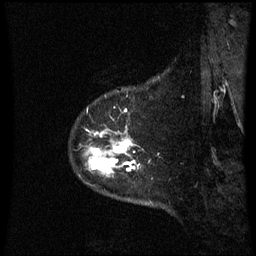
Breast MRI (dynamic contrast-enhanced), one sagittal slice; position 54 of 60 along the scan axis; dynamic contrast-enhanced series, image 2 of 3 at this slice position (ordered by acquisition); 1.5 T; TE 4.2 ms, TR 8.9 ms; 2.3 mm slice thickness; 256 × 256 image matrix, field of view 210 × 210 mm. Patient: female, 43 years. From the clinical record (not read from this slice): setting: breast cancer imaged before/during neoadjuvant chemotherapy; receptor status: HER2-positive.
Outlined on this slice (semi-automatic segmentation, software-assisted and operator-edited):
- analysis volume of interest (the breast-tissue region the enhancement analysis was run in; not a lesion): bounding box <80,109,160,179> (left, top, right, bottom; pixels)
- tumour enhancement mask (voxels above the 70 % enhancement threshold inside the analysis volume of interest): <90,111,140,173>